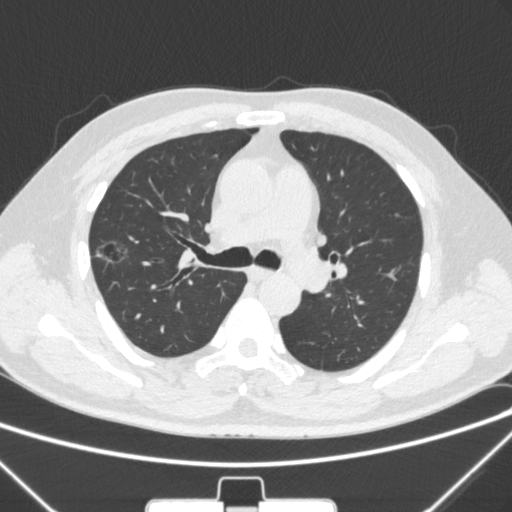
Chest CT, one axial slice. Slice 198 of 320 in the series (ordered by position). Lung window (W 1500 / L -600 HU). 1 mm slice thickness. 512 × 512 image matrix. Patient: male, 58 years. Case-level facts recorded for this patient, not image findings: clinical TNM (as recorded): T1c N0 M0.
Outlined on this slice (bounding box drawn by a radiologist):
- lung tumour (recorded histology: adenocarcinoma): bounding box (x1, y1, x2, y2) in pixels: (92, 225, 143, 281)